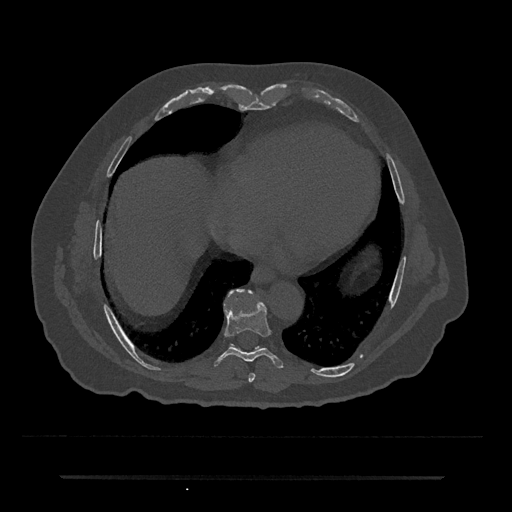
CT including the spine, one axial slice; slice 324 of 797 in the series (ordered by position); reconstruction kernel Br40s/3; bone window (W 1800 / L 400 HU); 0.5 mm slice thickness; 512 × 512 image matrix, field of view 437 × 437 mm. Male patient, age 69 years. From the clinical record (not read from this slice): primary cancer: prostate.
Annotated regions visible in this slice (semi-automatic segmentation, software-assisted and operator-edited):
- T7 vertebra: bounding box [x1, y1, x2, y2] px = [248, 373, 256, 382]
- T8 vertebra: [214, 301, 284, 368]
- T9 vertebra: [231, 289, 245, 293]